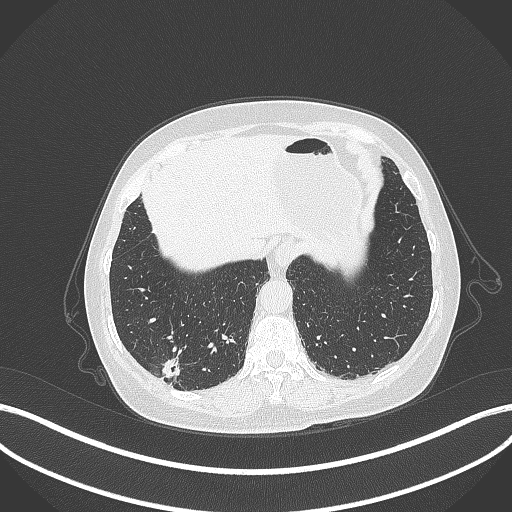
Chest CT, one axial slice; position 54 of 333 along the scan axis; lung window (W 1500 / L -600 HU); 1 mm slice thickness; 512 × 512 image matrix, field of view 400 × 400 mm. Female patient, age 69 years. Case-level facts recorded for this patient, not image findings: clinical TNM (as recorded): T1b N0 M0.
Annotated regions visible in this slice (bounding box drawn by a radiologist):
- lung tumour (recorded histology: adenocarcinoma): box from (x=158, y=352) to (x=181, y=379) px